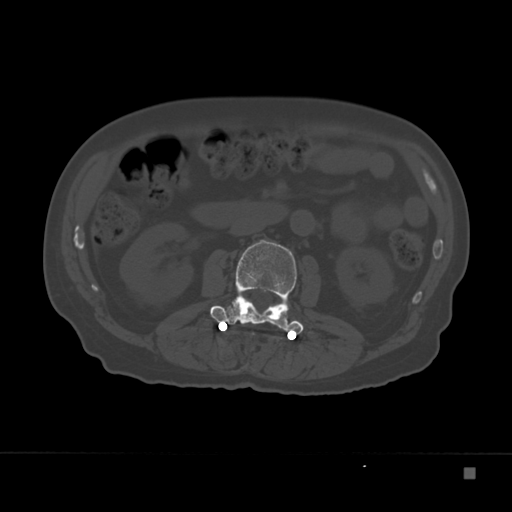
CT including the spine, one axial slice; position 87 of 332 along the scan axis; reconstruction kernel Br40s; bone window (W 1800 / L 400 HU); 1.5 mm slice thickness; 512 × 512 image matrix, field of view 389 × 389 mm. Patient: male, 72 years. Case-level facts recorded for this patient, not image findings: primary cancer: skeletal.
Annotated regions visible in this slice (semi-automatically segmented with operator editing):
- L2 vertebra: bounding box (x1, y1, x2, y2) in pixels: (211, 239, 304, 334)
- L3 vertebra: (225, 322, 235, 325)